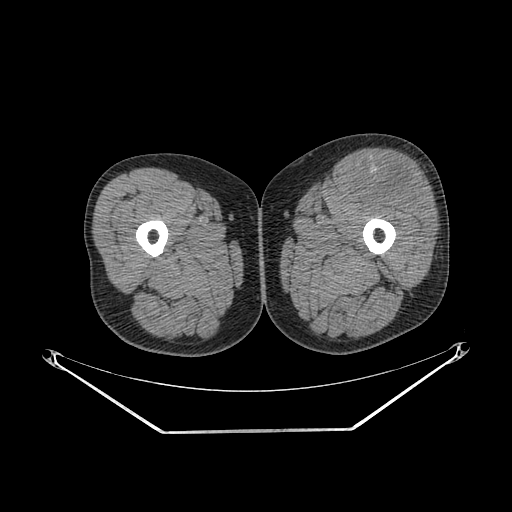
CT of an extremity soft-tissue mass (from a PET/CT study), one axial slice. Position 231 of 267 along the scan axis. Reconstruction kernel SOFT. Soft-tissue window (W 400 / L 40 HU). 3.75 mm slice thickness. 512 × 512 image matrix, field of view 500 × 500 mm. Male patient. From the clinical record (not read from this slice): histological type: extraskeletal osteosarcoma; grade: high; site of the primary tumour: thigh.
Structures marked on this image (expert contour drawn on MRI and transferred to this co-registered scan by the dataset authors):
- gross tumour volume (mass): bounding box (x1, y1, x2, y2) in pixels: (358, 162, 428, 211)